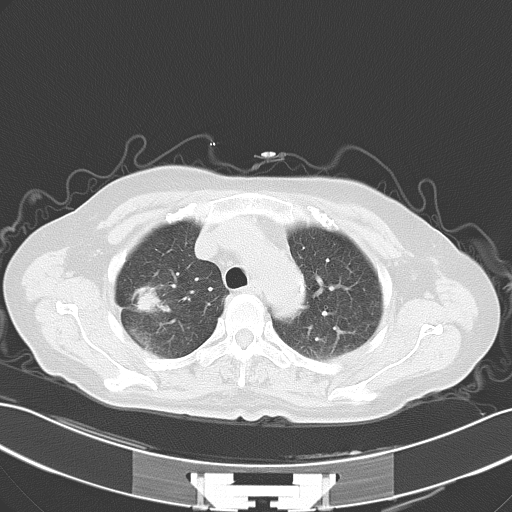
Chest CT, one axial slice. Position 44 of 57 along the scan axis. Reconstruction kernel B70f. 120 kVp. Lung window (W 1500 / L -600 HU). 512 × 512 image matrix. Patient: female, 65 years. From the clinical record (not read from this slice): clinical TNM (as recorded): T1c N0 M1c.
Outlined on this slice (rectangle marked by the reading radiologist):
- lung tumour (recorded histology: adenocarcinoma): bounding box (x1, y1, x2, y2) in pixels: (134, 280, 166, 318)